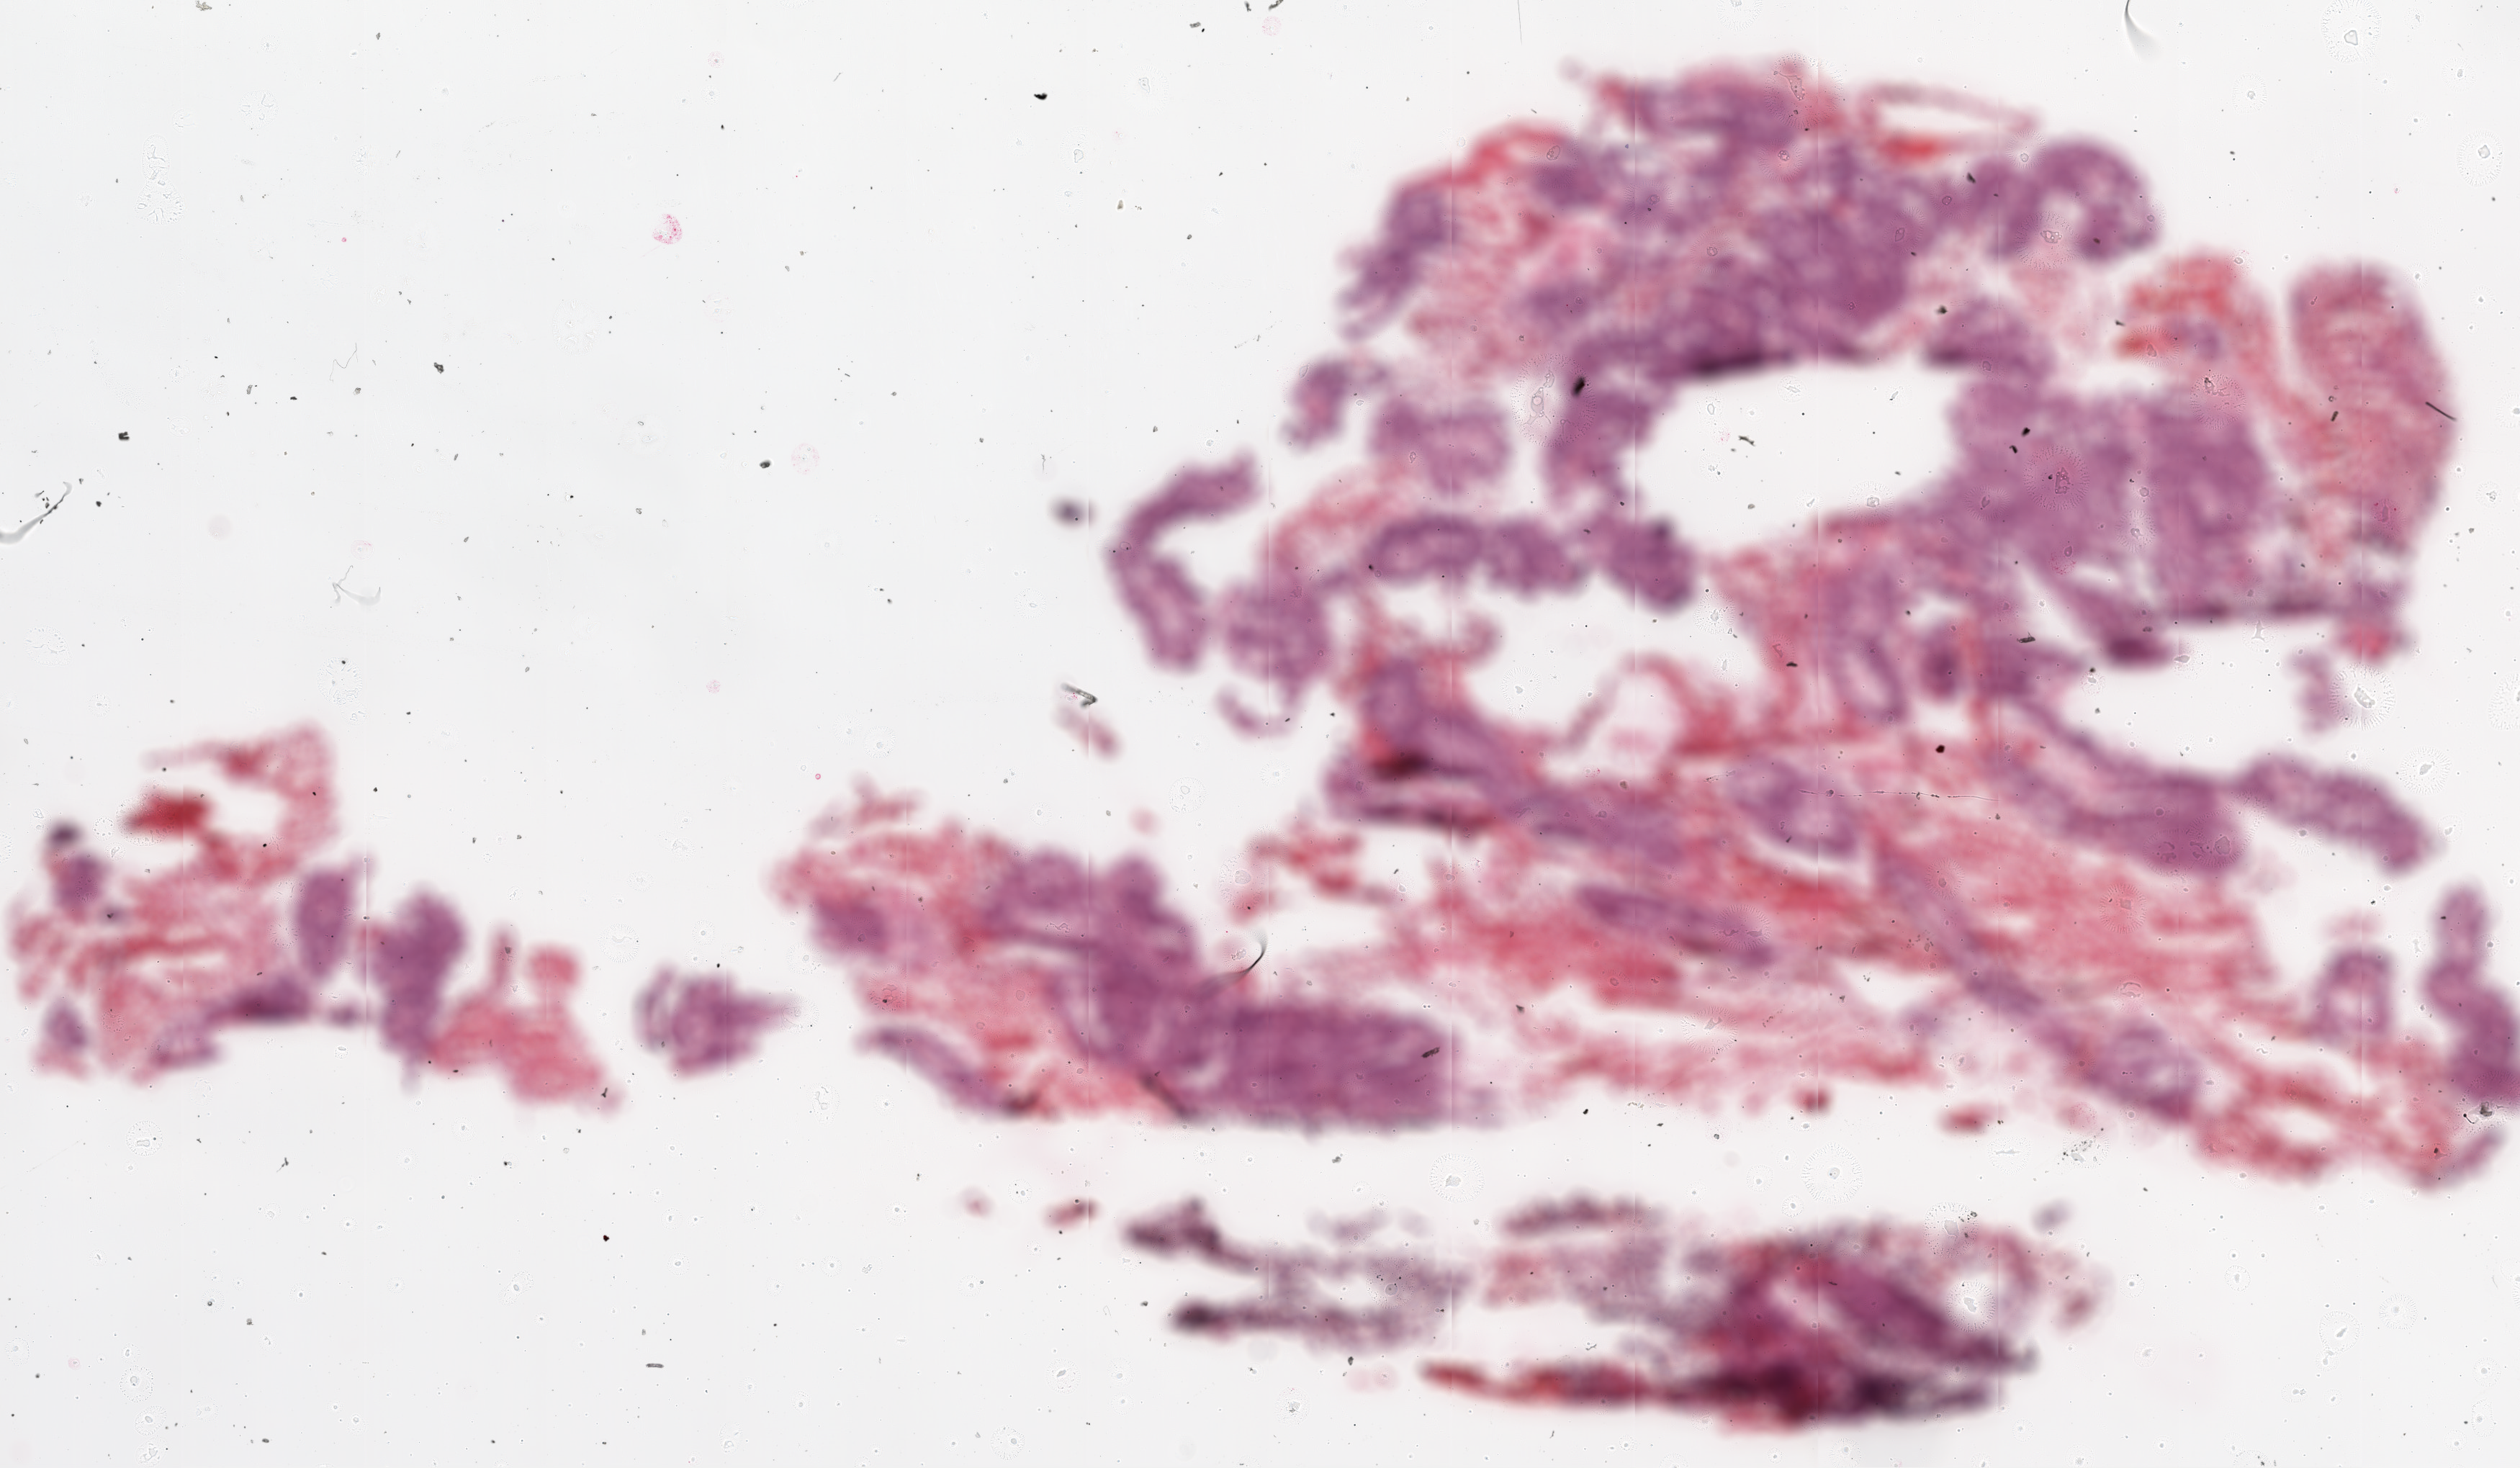
H&E-stained whole-slide image, whole scanned area (about 14.0 x 8.2 mm, acquisition: 20x scan) shown as a low-resolution overview. Frozen section from the top of the tissue portion. Sample: recurrent tumour, ovary. Patient: female, age at initial diagnosis 58 years. Composition of this section per pathologist review: tumour cells 60%, tumour nuclei 90%, normal cells 0%, stromal cells 20%, necrosis 20%.
This section: recurrent tumour. Patient diagnosis: Serous cystadenocarcinoma, NOS.